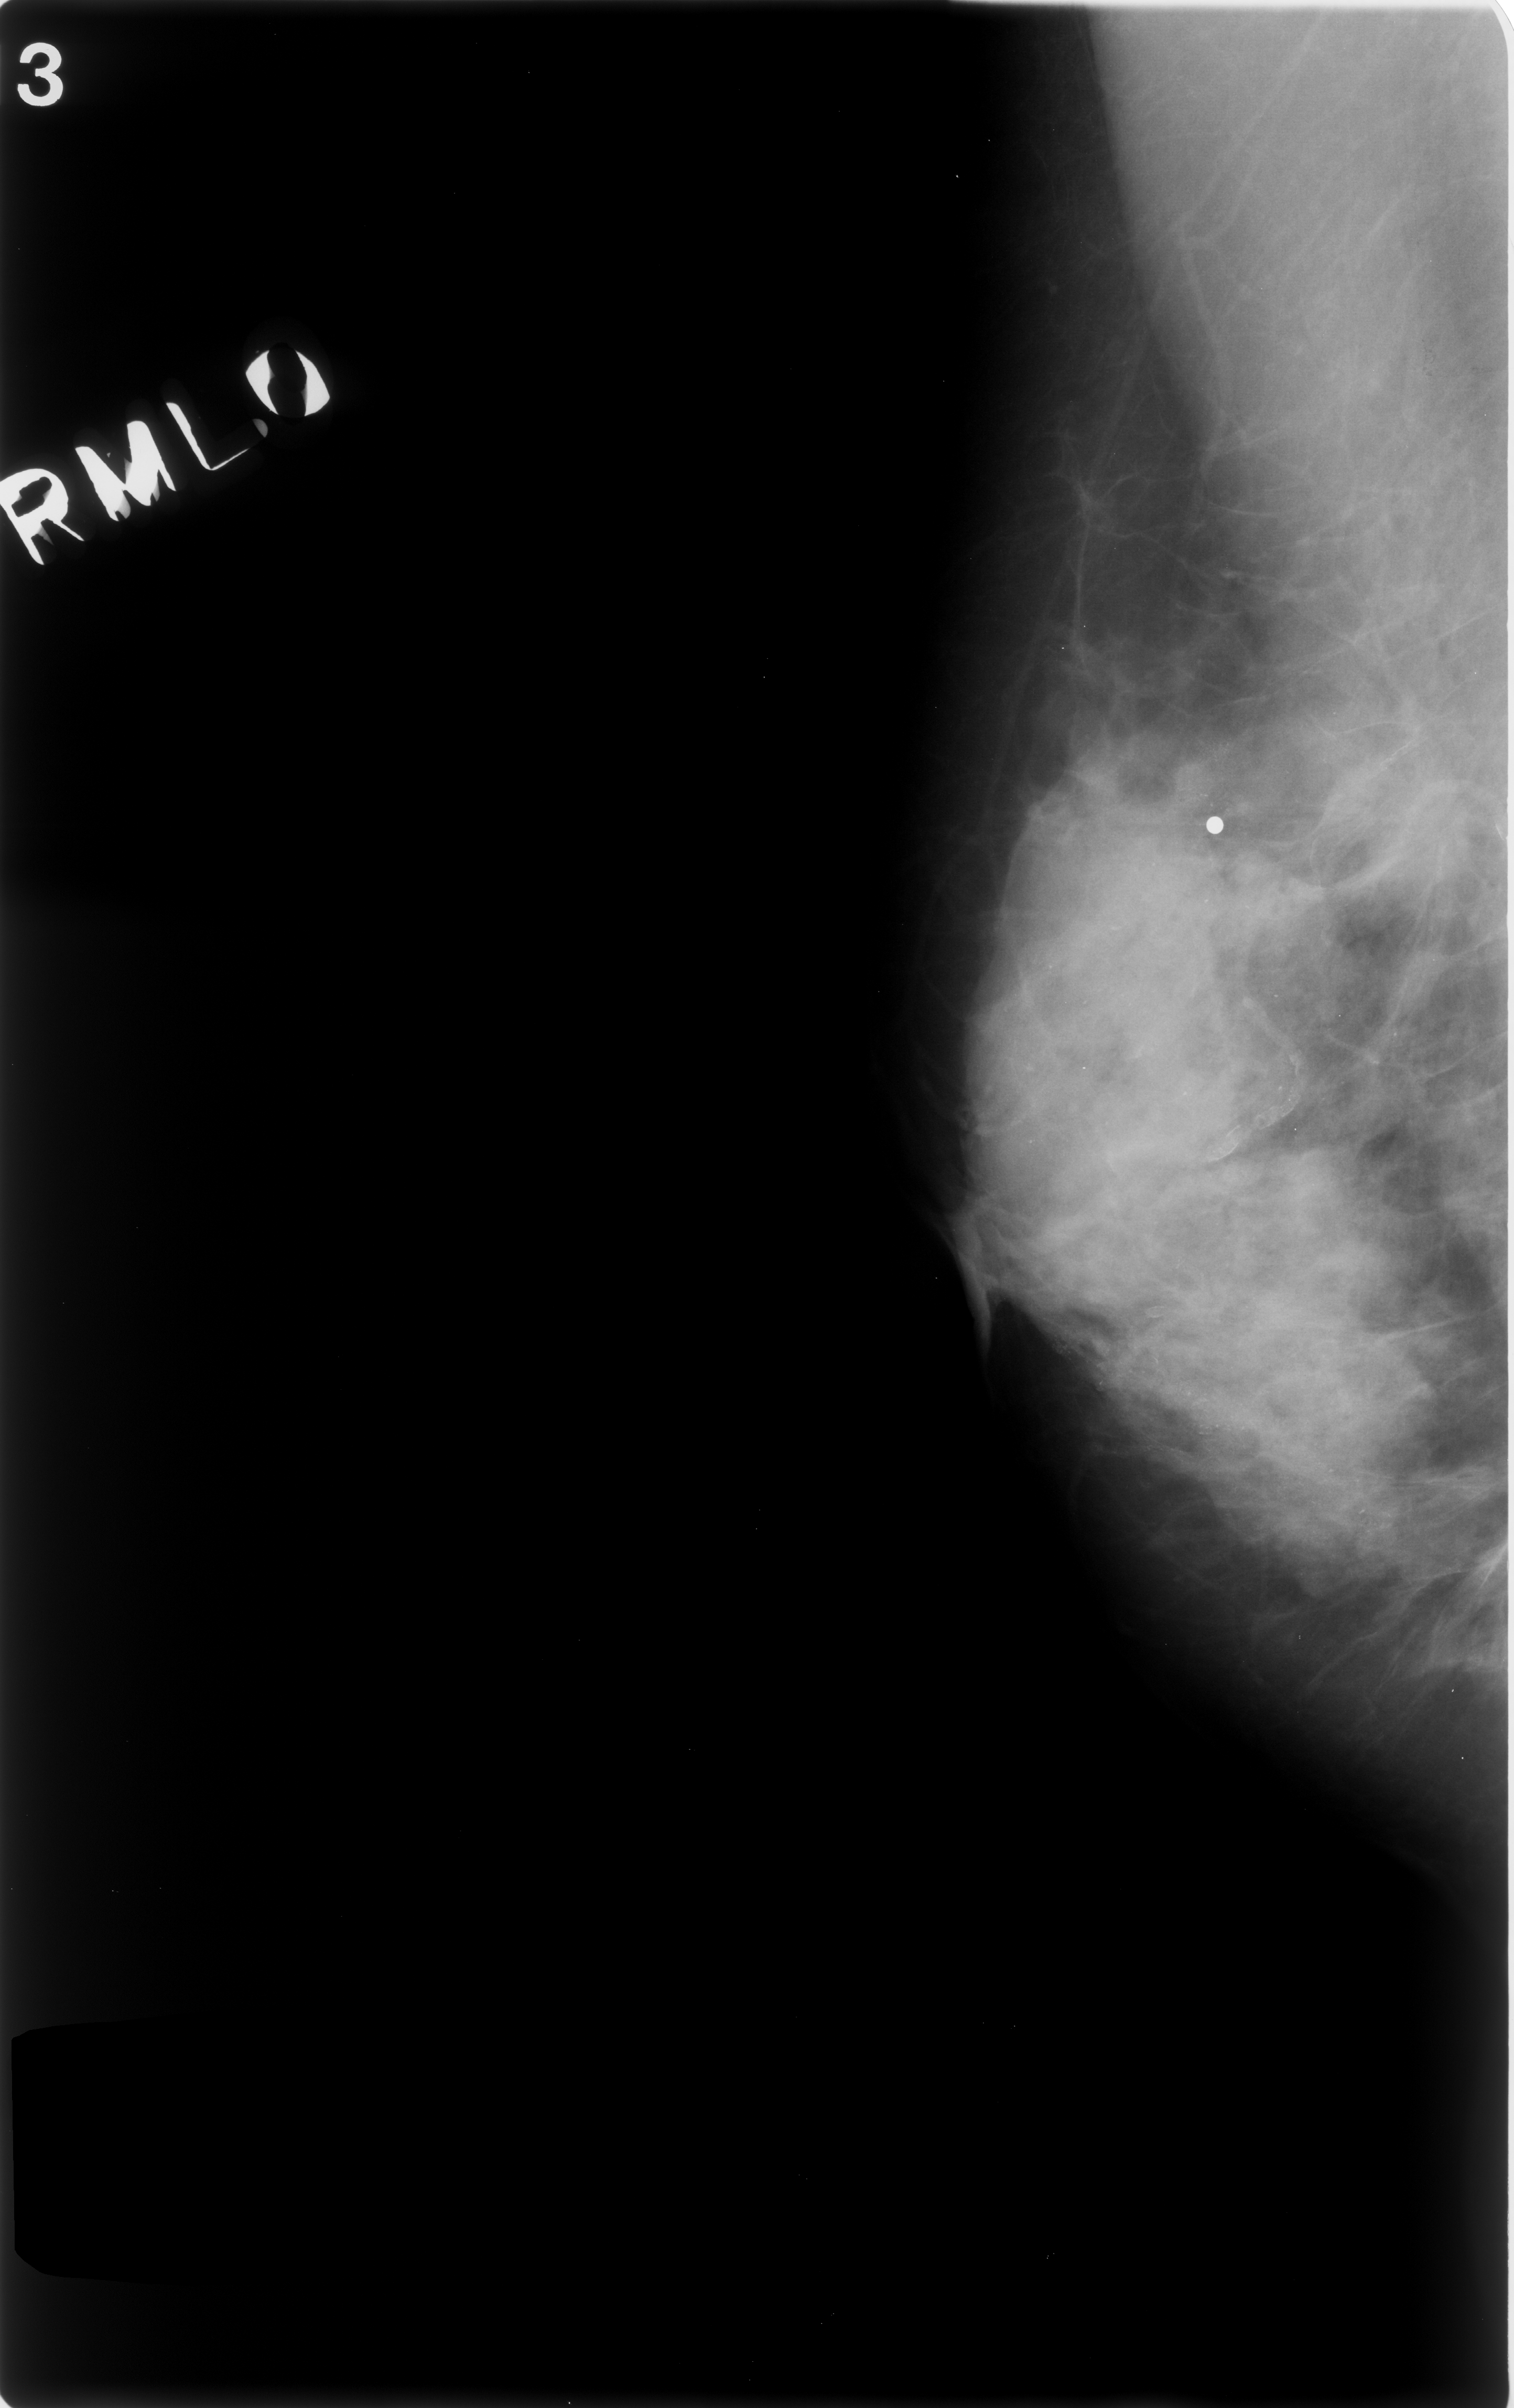
Mammogram (digitized film); right breast; mediolateral oblique (MLO) view; breast composition: extremely dense (BI-RADS density category 4 of 4).
Marked findings (only marked abnormalities are described; nothing is implied about the rest of the image): mass, shape architectural distortion, margins spiculated; BI-RADS assessment category 5; pathology (as recorded): malignant.